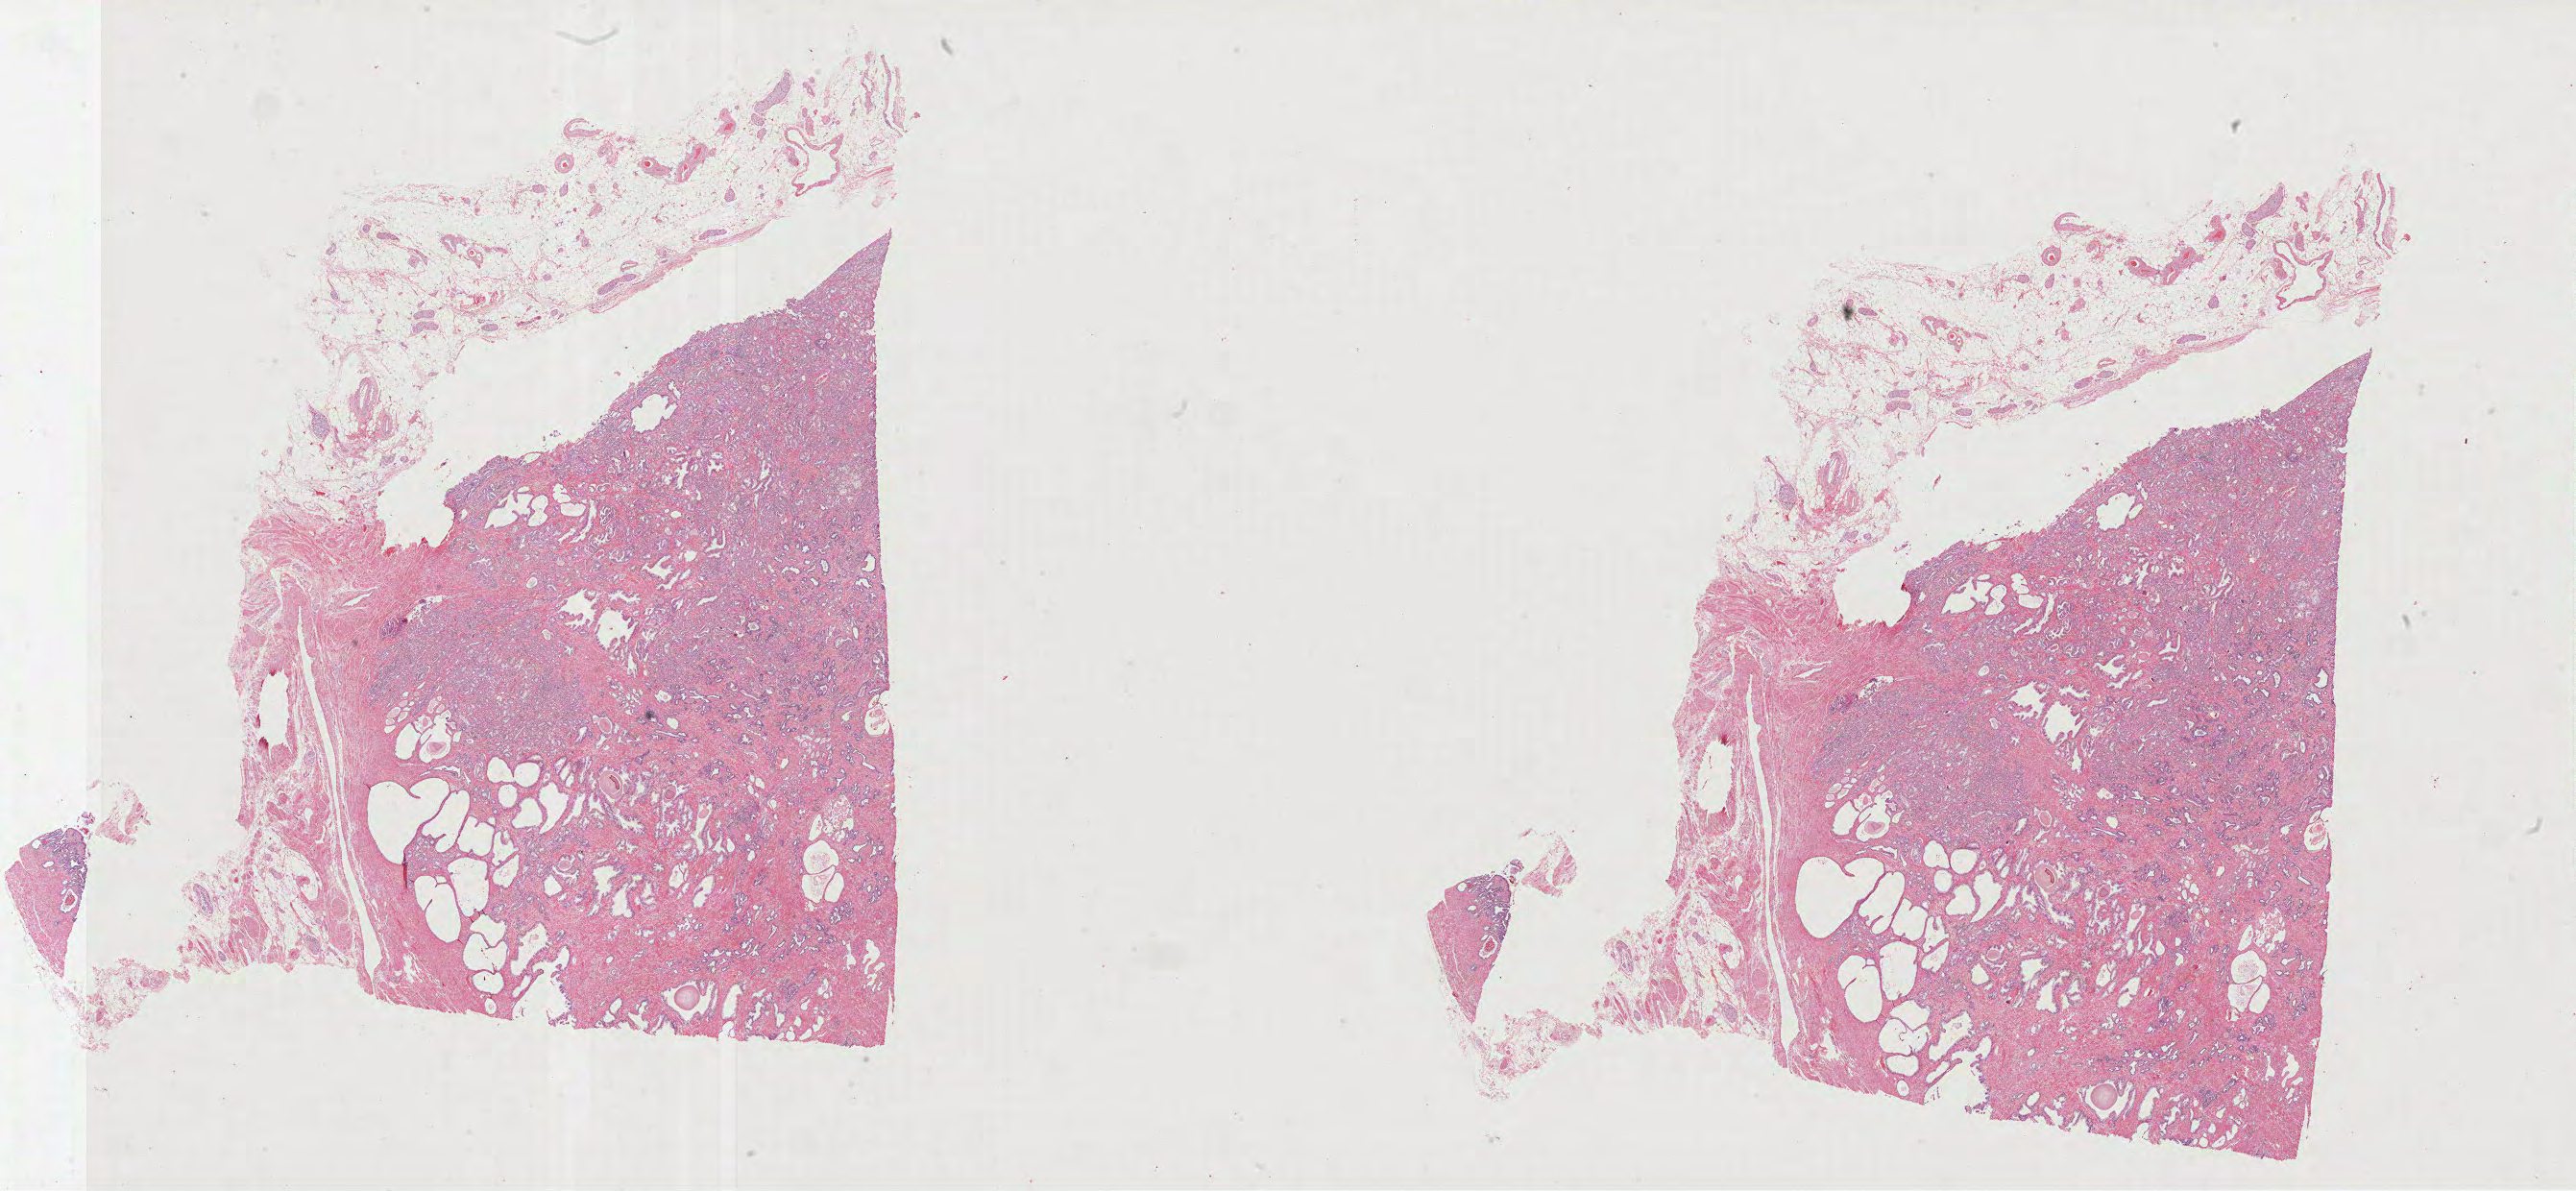
Whole-slide histology image, H&E, shown as a low-resolution overview of the whole scanned area (about 43.3 x 20.0 mm, from a 40x scan). Formalin-fixed paraffin-embedded (FFPE) diagnostic section. Prostate, primary tumour sample. Patient: male, age at initial diagnosis 72 years. Gleason score: 7 (3+4).
Laterality: bilateral. Lymph nodes positive (case pathology): 0 of 25 examined. Histologic diagnosis: Acinar cell carcinoma (prostate gland).